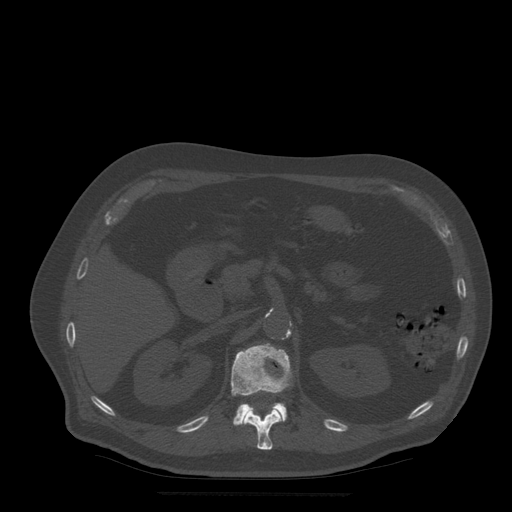
CT including the spine, one axial slice; position 207 of 522 along the scan axis; bone window (W 1800 / L 400 HU); 1.25 mm slice thickness; 512 × 512 image matrix. Patient age 72 years. From the clinical record (not read from this slice): primary cancer: prostate.
Outlined on this slice (semi-automatically segmented with operator editing):
- L1 vertebra: bounding box (x1, y1, x2, y2) in pixels: (231, 344, 291, 426)
- T12 vertebra: (244, 408, 283, 450)